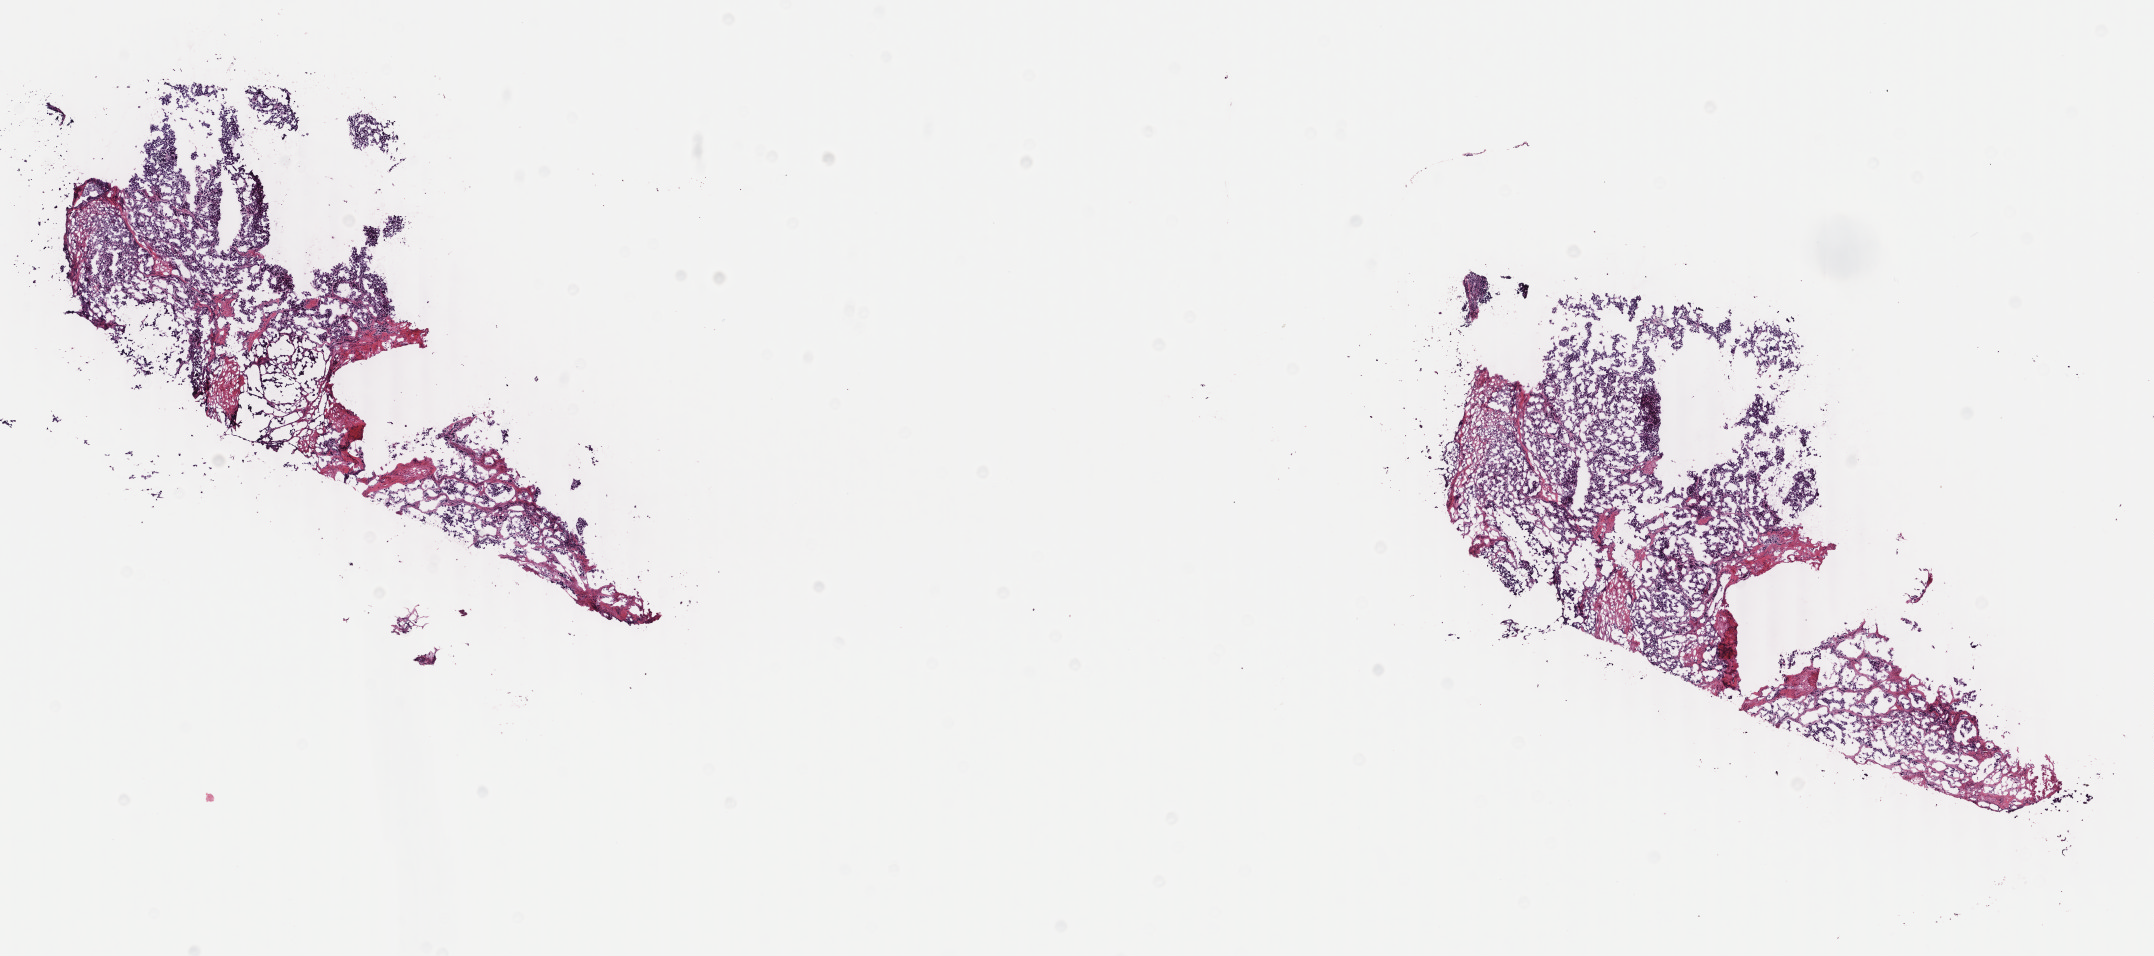
Hematoxylin and eosin (H&E) stained whole-slide image, a low-resolution overview of the entire scanned area, about 17.1 x 7.6 mm, frozen section from the top of the tissue portion, metastatic tumour sample, sampled site: lymph nodes of axilla or arm. Patient: female, age at initial diagnosis 46 years. Composition of this section per pathologist review: tumour cells 80%, tumour nuclei 80%, normal cells 0%, stromal cells 19%, necrosis 1%. Infiltration values recorded for this section: lymphocyte infiltration 2%, monocyte infiltration 1%, neutrophil infiltration 1%.
* this section: metastatic tumour tissue
* patient diagnosis: Malignant melanoma, NOS